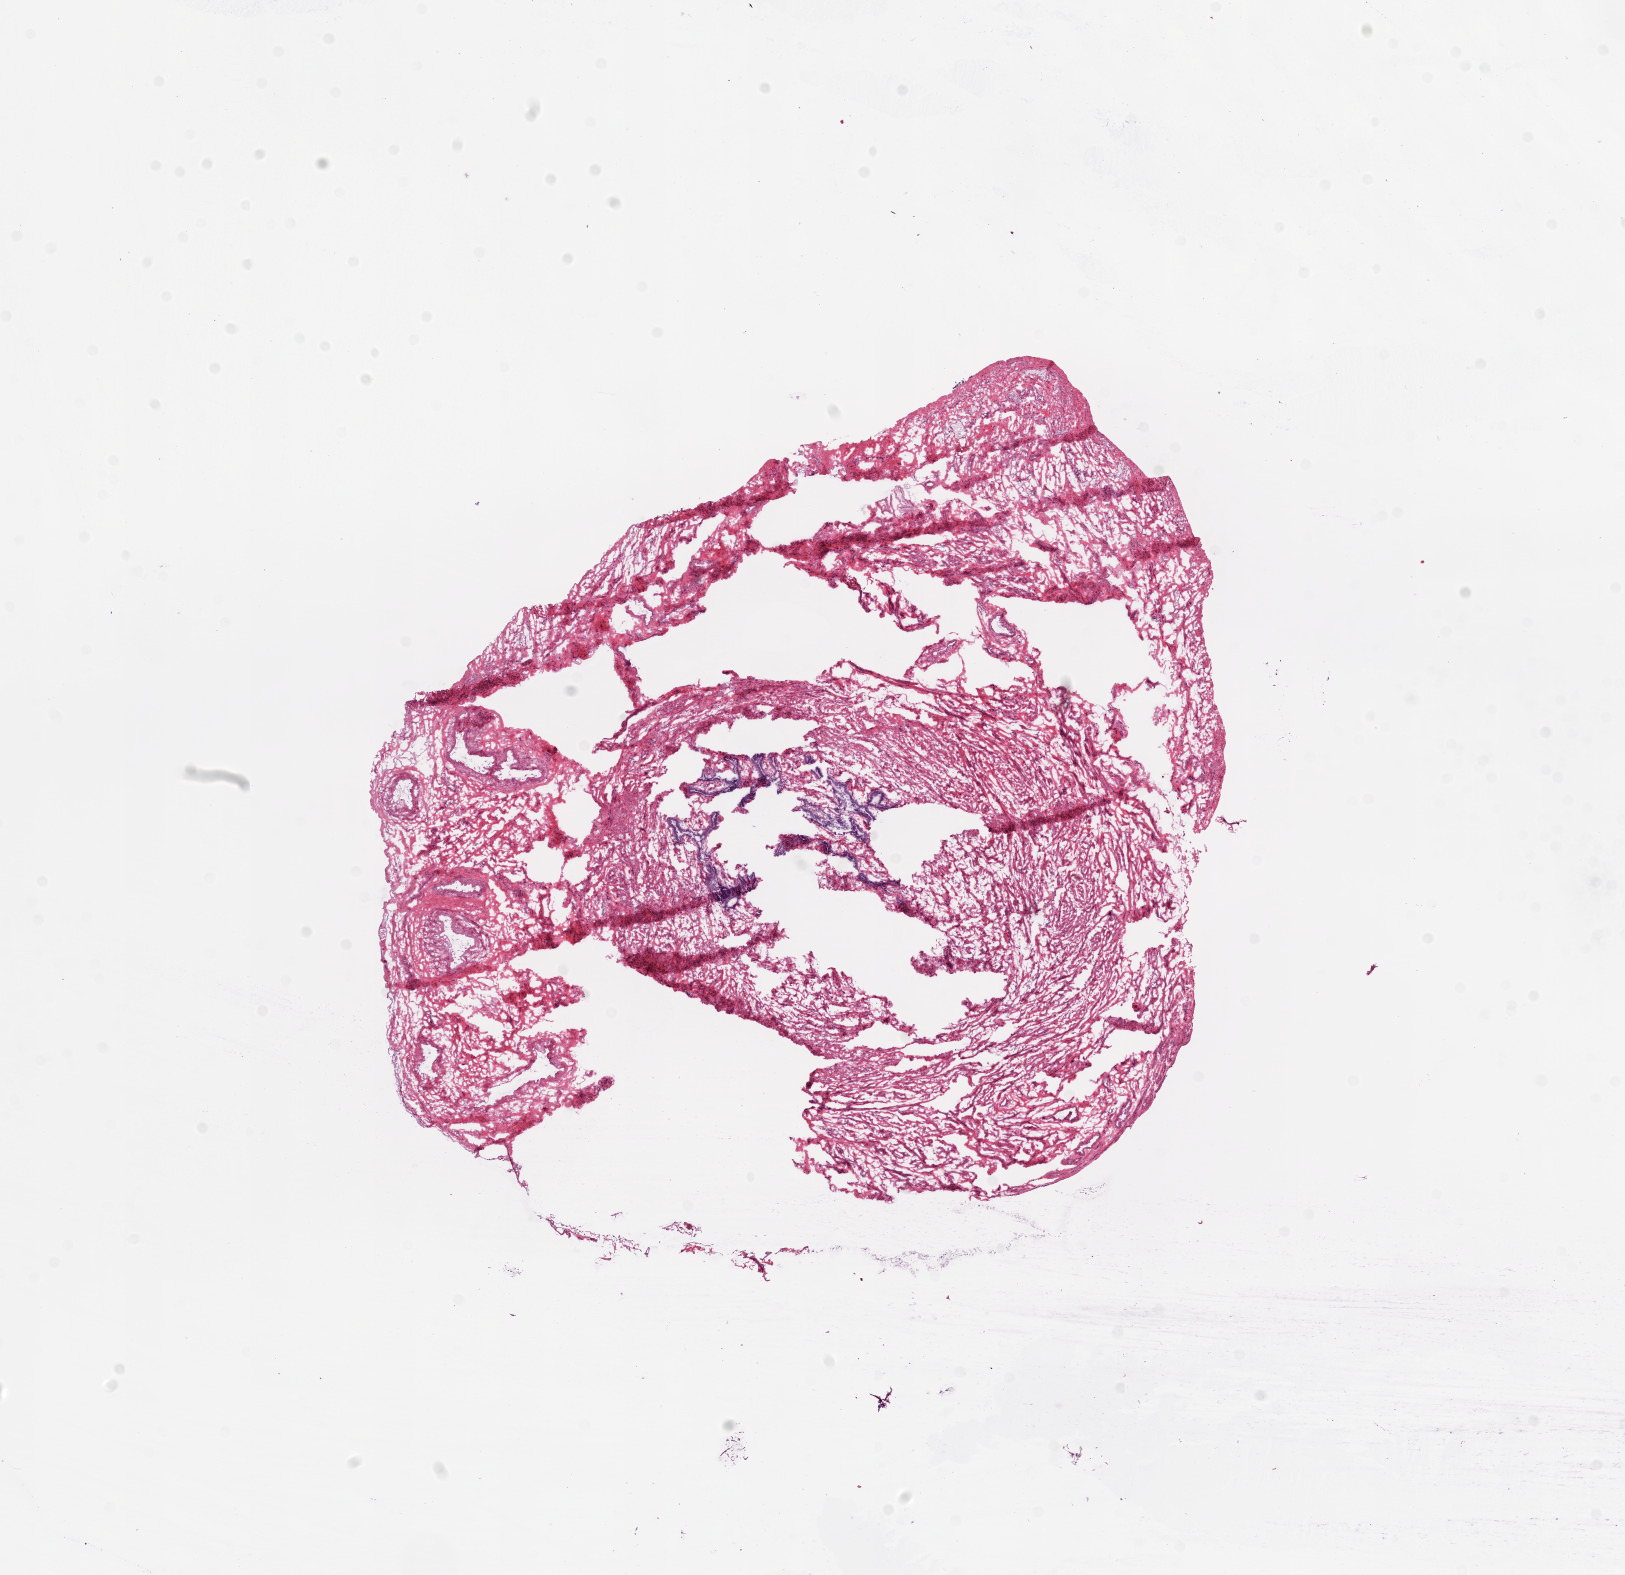
Whole-slide histology image, H&E-stained, whole scanned area (about 13.0 x 12.6 mm) shown as a low-resolution overview; frozen section from the bottom of the tissue portion; sample: solid tissue normal (non-tumour tissue), ovary. Female, age 61 years at initial diagnosis.
This section: solid tissue normal (non-tumour) sample from the same patient. Patient diagnosis: Serous cystadenocarcinoma, NOS.